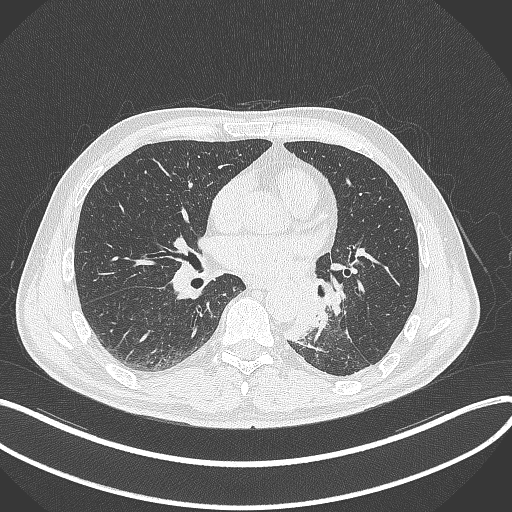
Chest CT, one axial slice; position 156 of 329 along the scan axis; 120 kVp; lung window (W 1500 / L -600 HU); 512 × 512 image matrix, field of view 400 × 400 mm. Patient: male, 59 years. From the clinical record (not read from this slice): clinical TNM (as recorded): T2a N2 M0.
Annotated regions visible in this slice (bounding box drawn by a radiologist):
- lung tumour (recorded histology: squamous cell carcinoma): bounding box <282,289,327,345> (left, top, right, bottom; pixels)